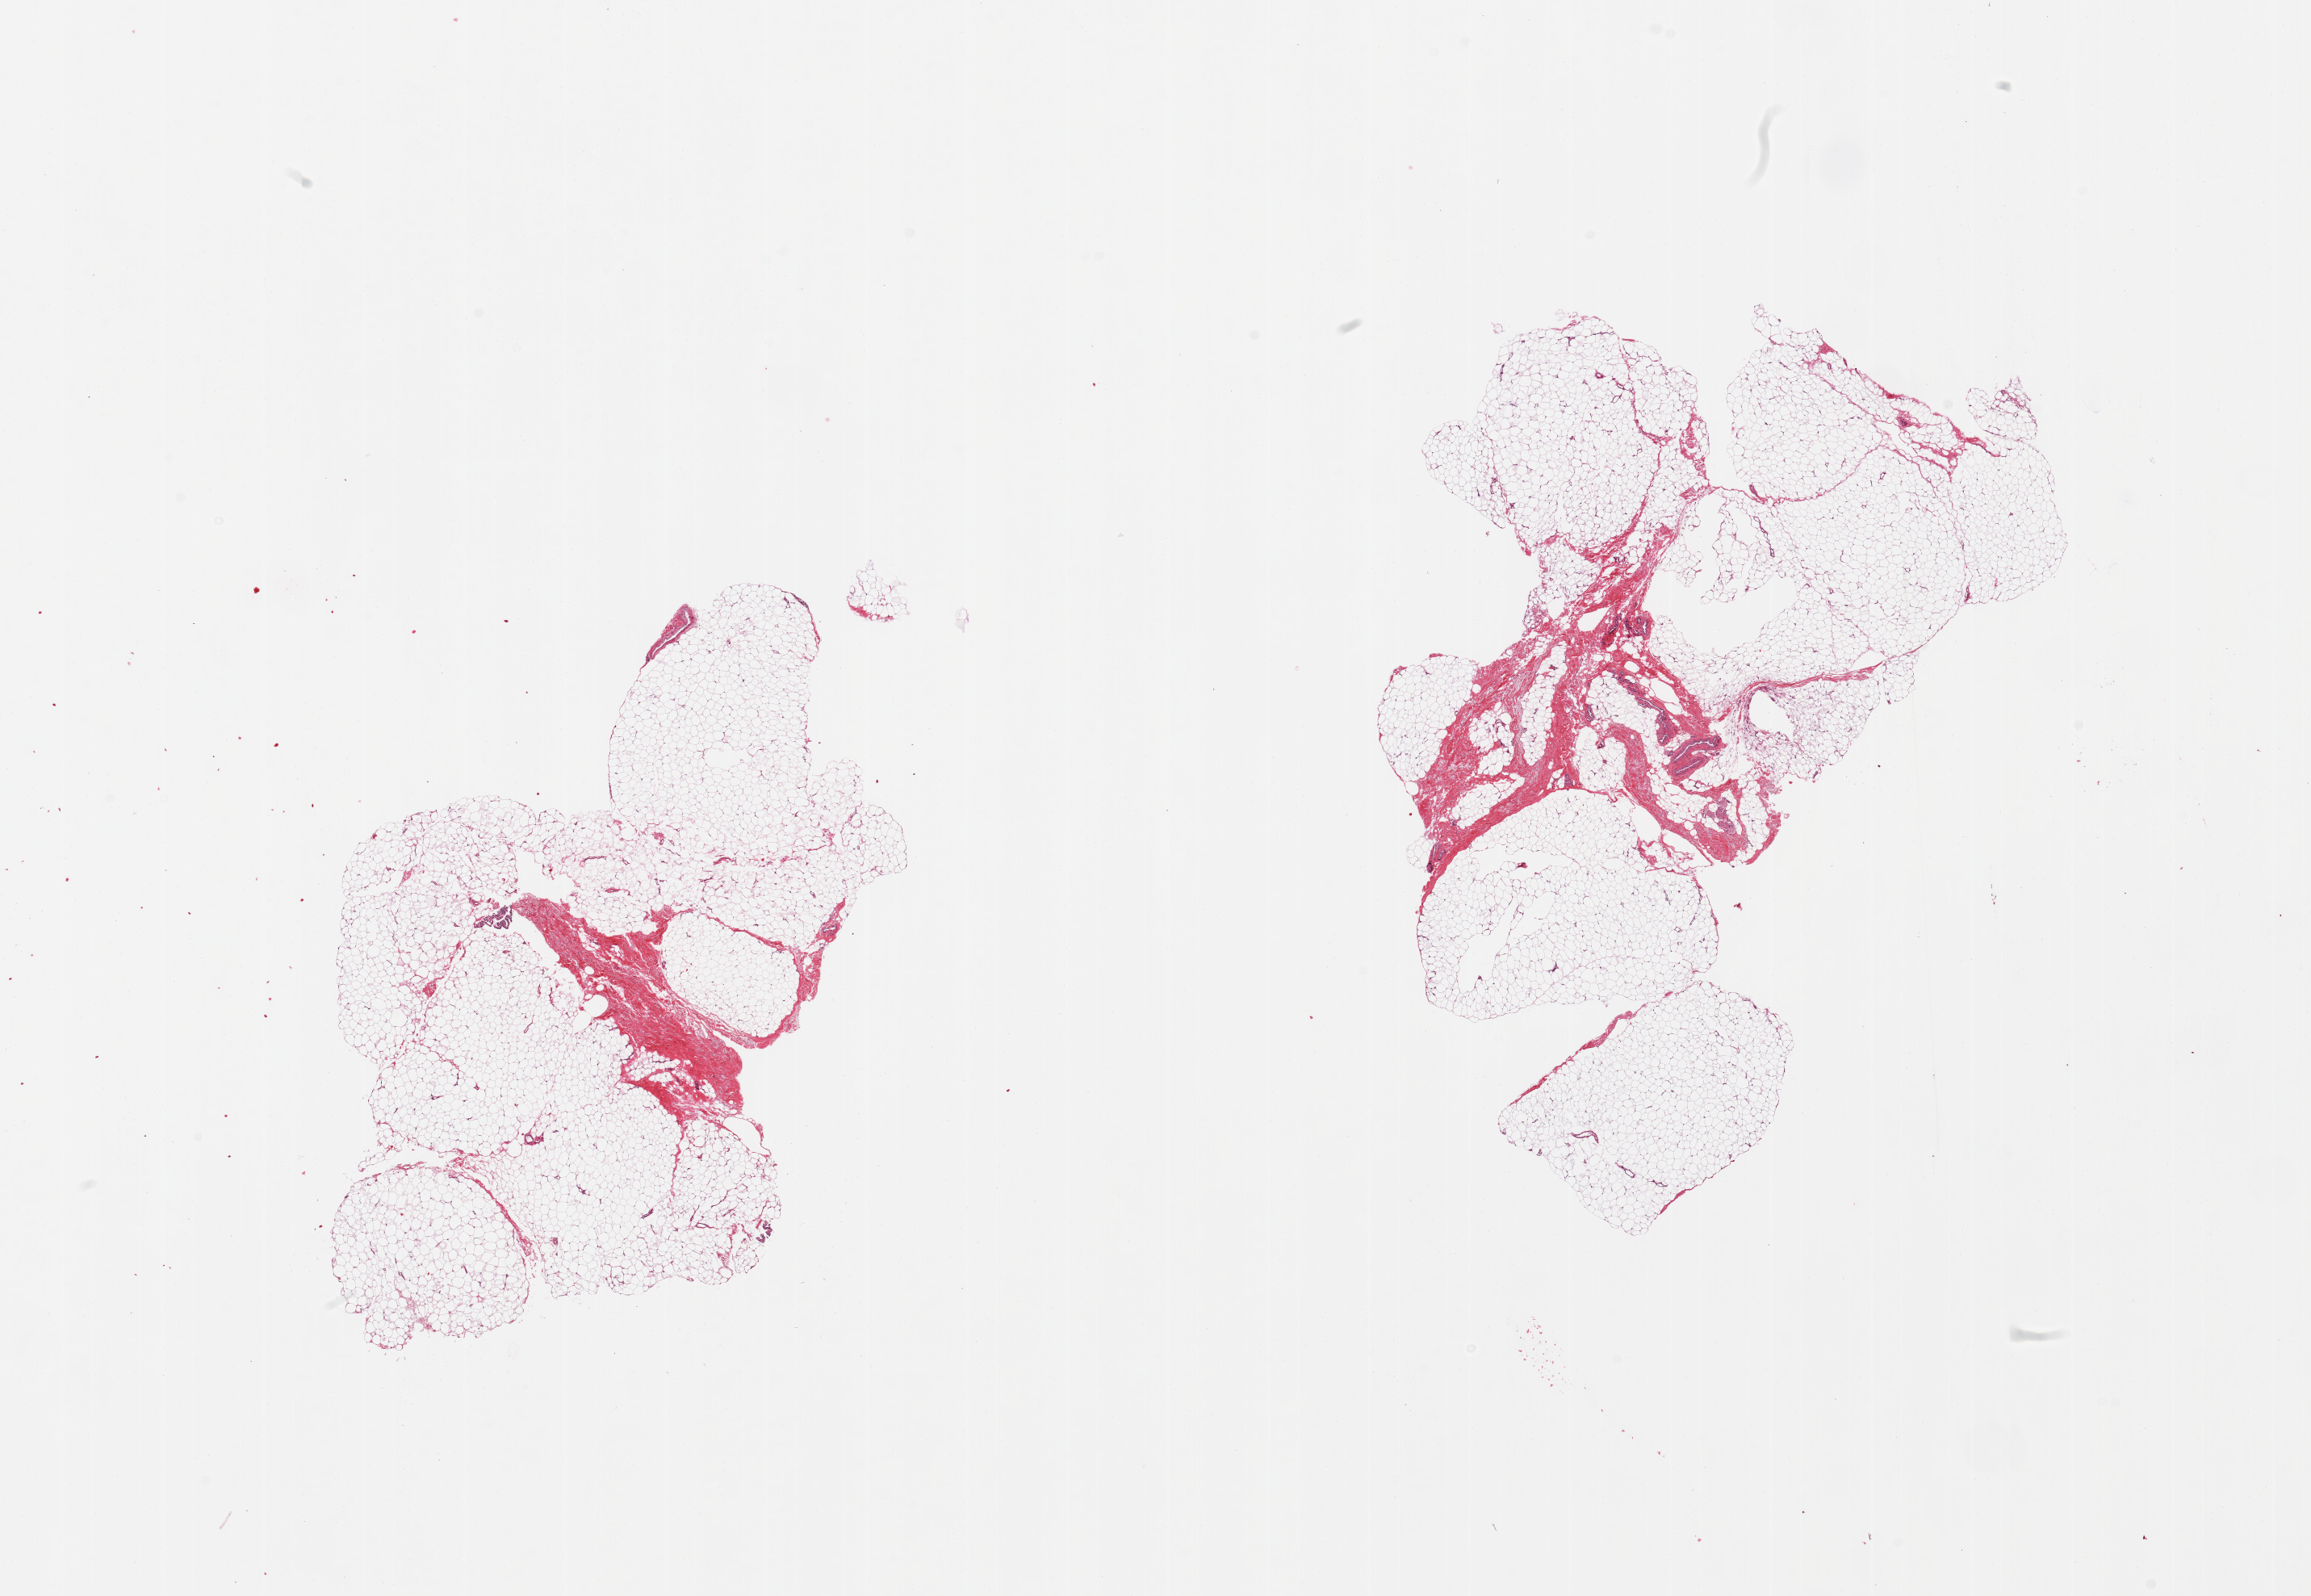
Hematoxylin and eosin (H&E) whole-slide image — shown as a low-resolution overview of the whole scanned area (about 22.6 x 15.6 mm). PAXgene-fixed, paraffin-embedded tissue. Target tissue: adipose tissue. Donor tissue sample. Donor: male.
Review note (as recorded): 2 pieces, fascia/vascular elements are ~10-20% of tissue.